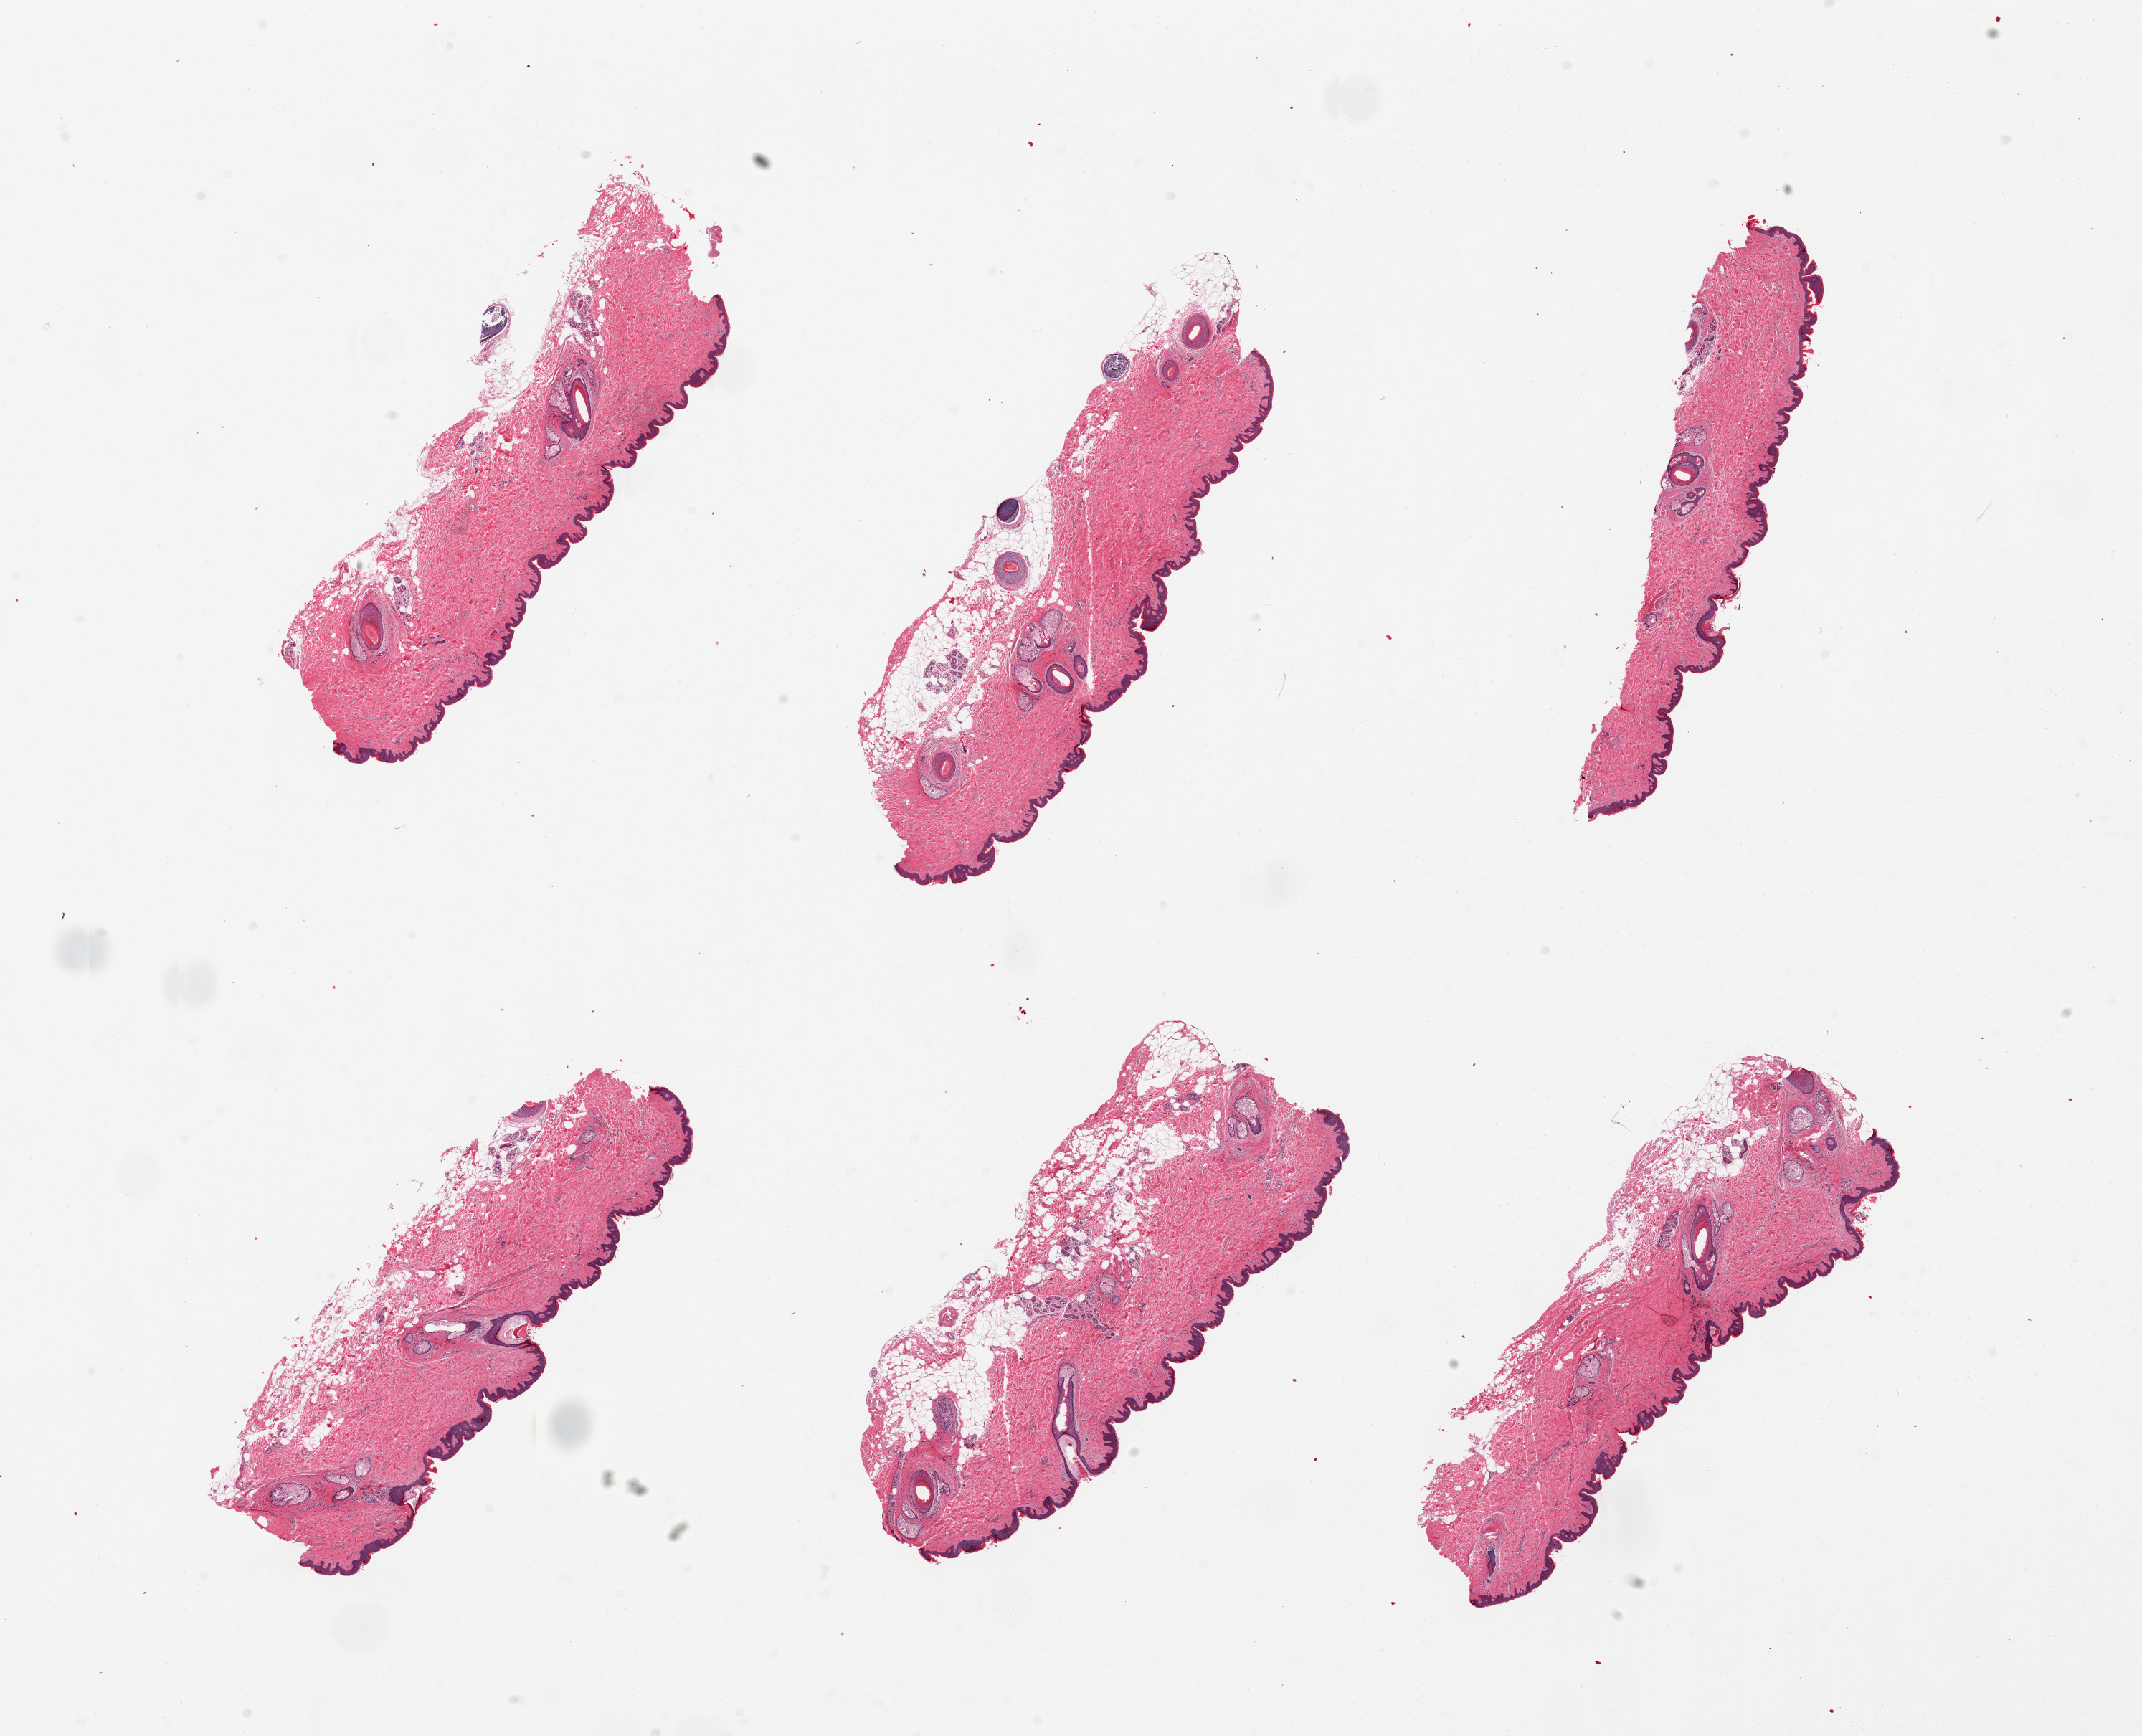
Digitized hematoxylin and eosin (H&E)-stained section — low-resolution overview of the scanned area, about 23.6 x 19.1 mm; PAXgene-fixed paraffin-embedded (PFPE) section; sampled site (target tissue): skin of suprapubic region; donor tissue sample. Donor: male.
Pathologist's review note for this sample: 6 pieces, squamous epithelium is ~50microns thick; minimal fat.